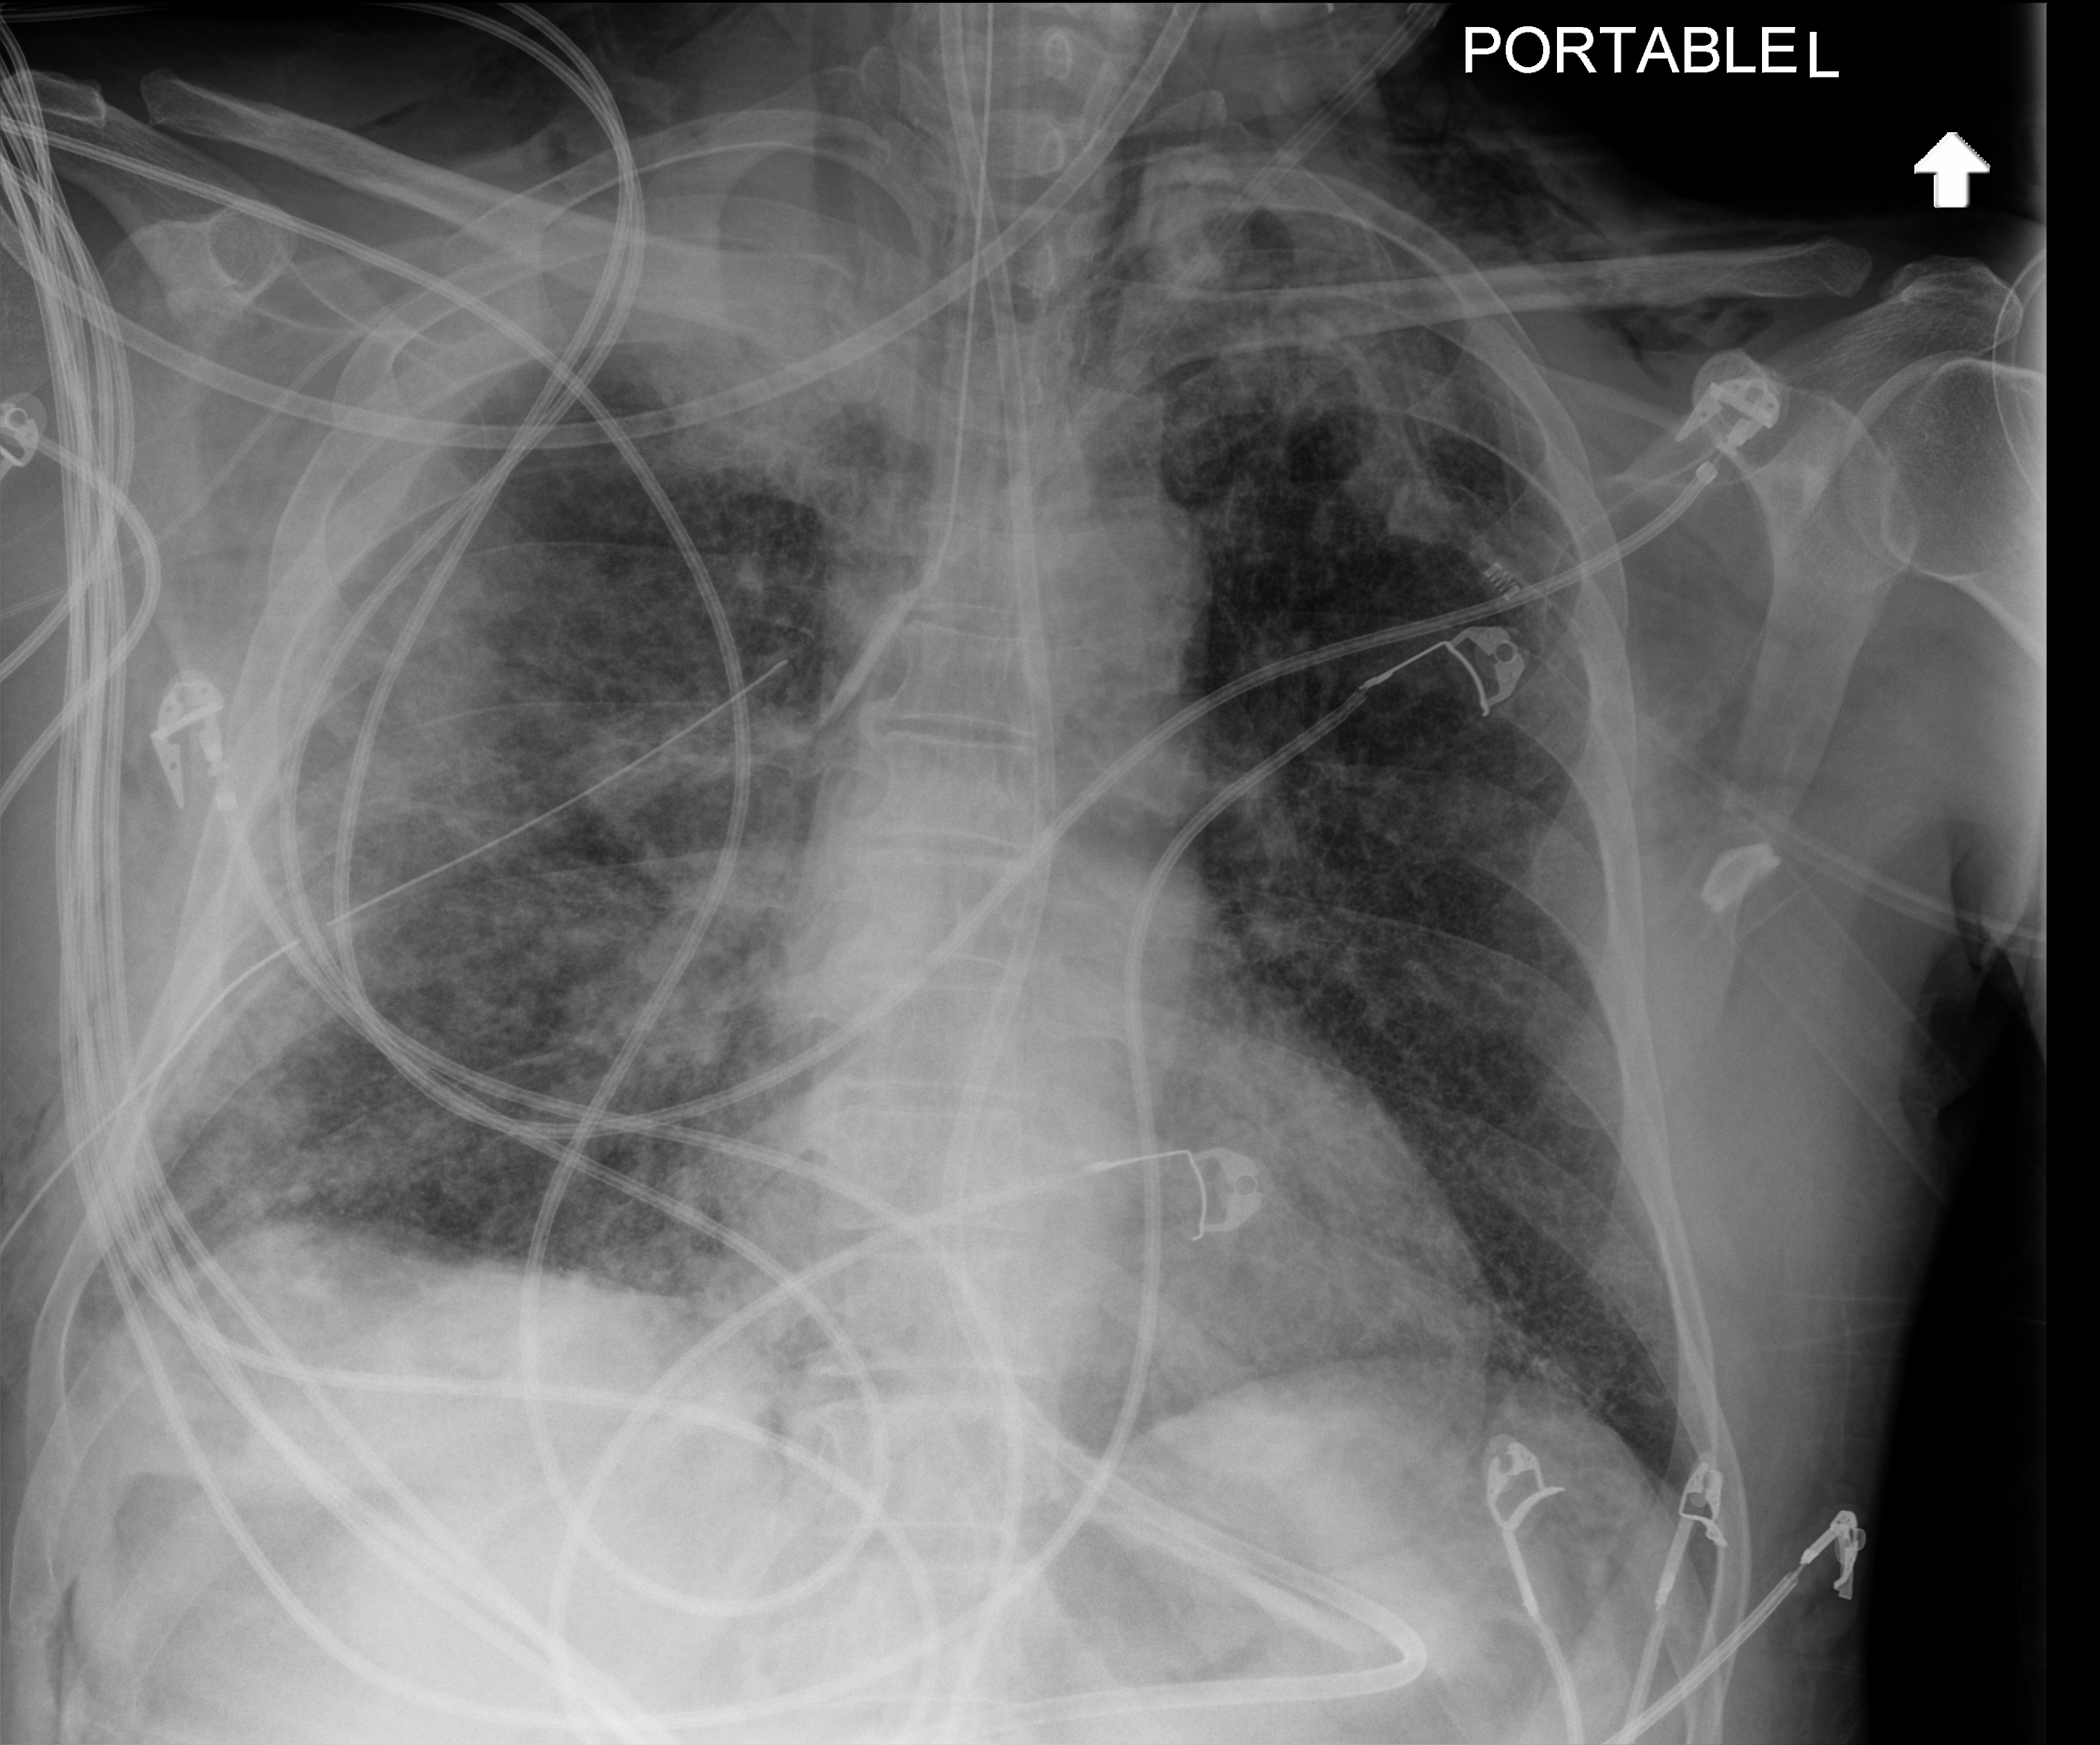
Portable chest radiograph; anteroposterior (AP) projection. Patient hospitalised with COVID-19; male, aged 18–59 years.
Hospital-stay facts (about this admission, not read from this image; timing relative to this image not recorded):
- mechanically ventilated during this hospital stay: yes
- smoking status (admission record): never